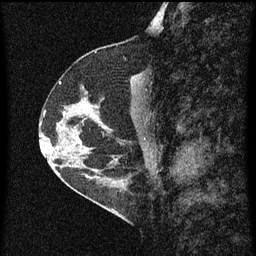
Breast MRI (dynamic contrast-enhanced), one sagittal slice; position 30 of 60 along the scan axis; dynamic contrast-enhanced series, image 2 of 3 at this slice position (ordered by acquisition); 1.5 T; TE 4.2 ms, TR 8 ms; 2 mm slice thickness; 256 × 256 image matrix. Female patient, age 56 years.
Structures marked on this image (semi-automatically segmented with operator editing):
- analysis volume of interest (the breast-tissue region the enhancement analysis was run in; not a lesion): box from (x=49, y=98) to (x=110, y=159) px
- tumour enhancement mask (voxels above the 70 % enhancement threshold inside the analysis volume of interest): (x=78, y=114)–(x=93, y=141)